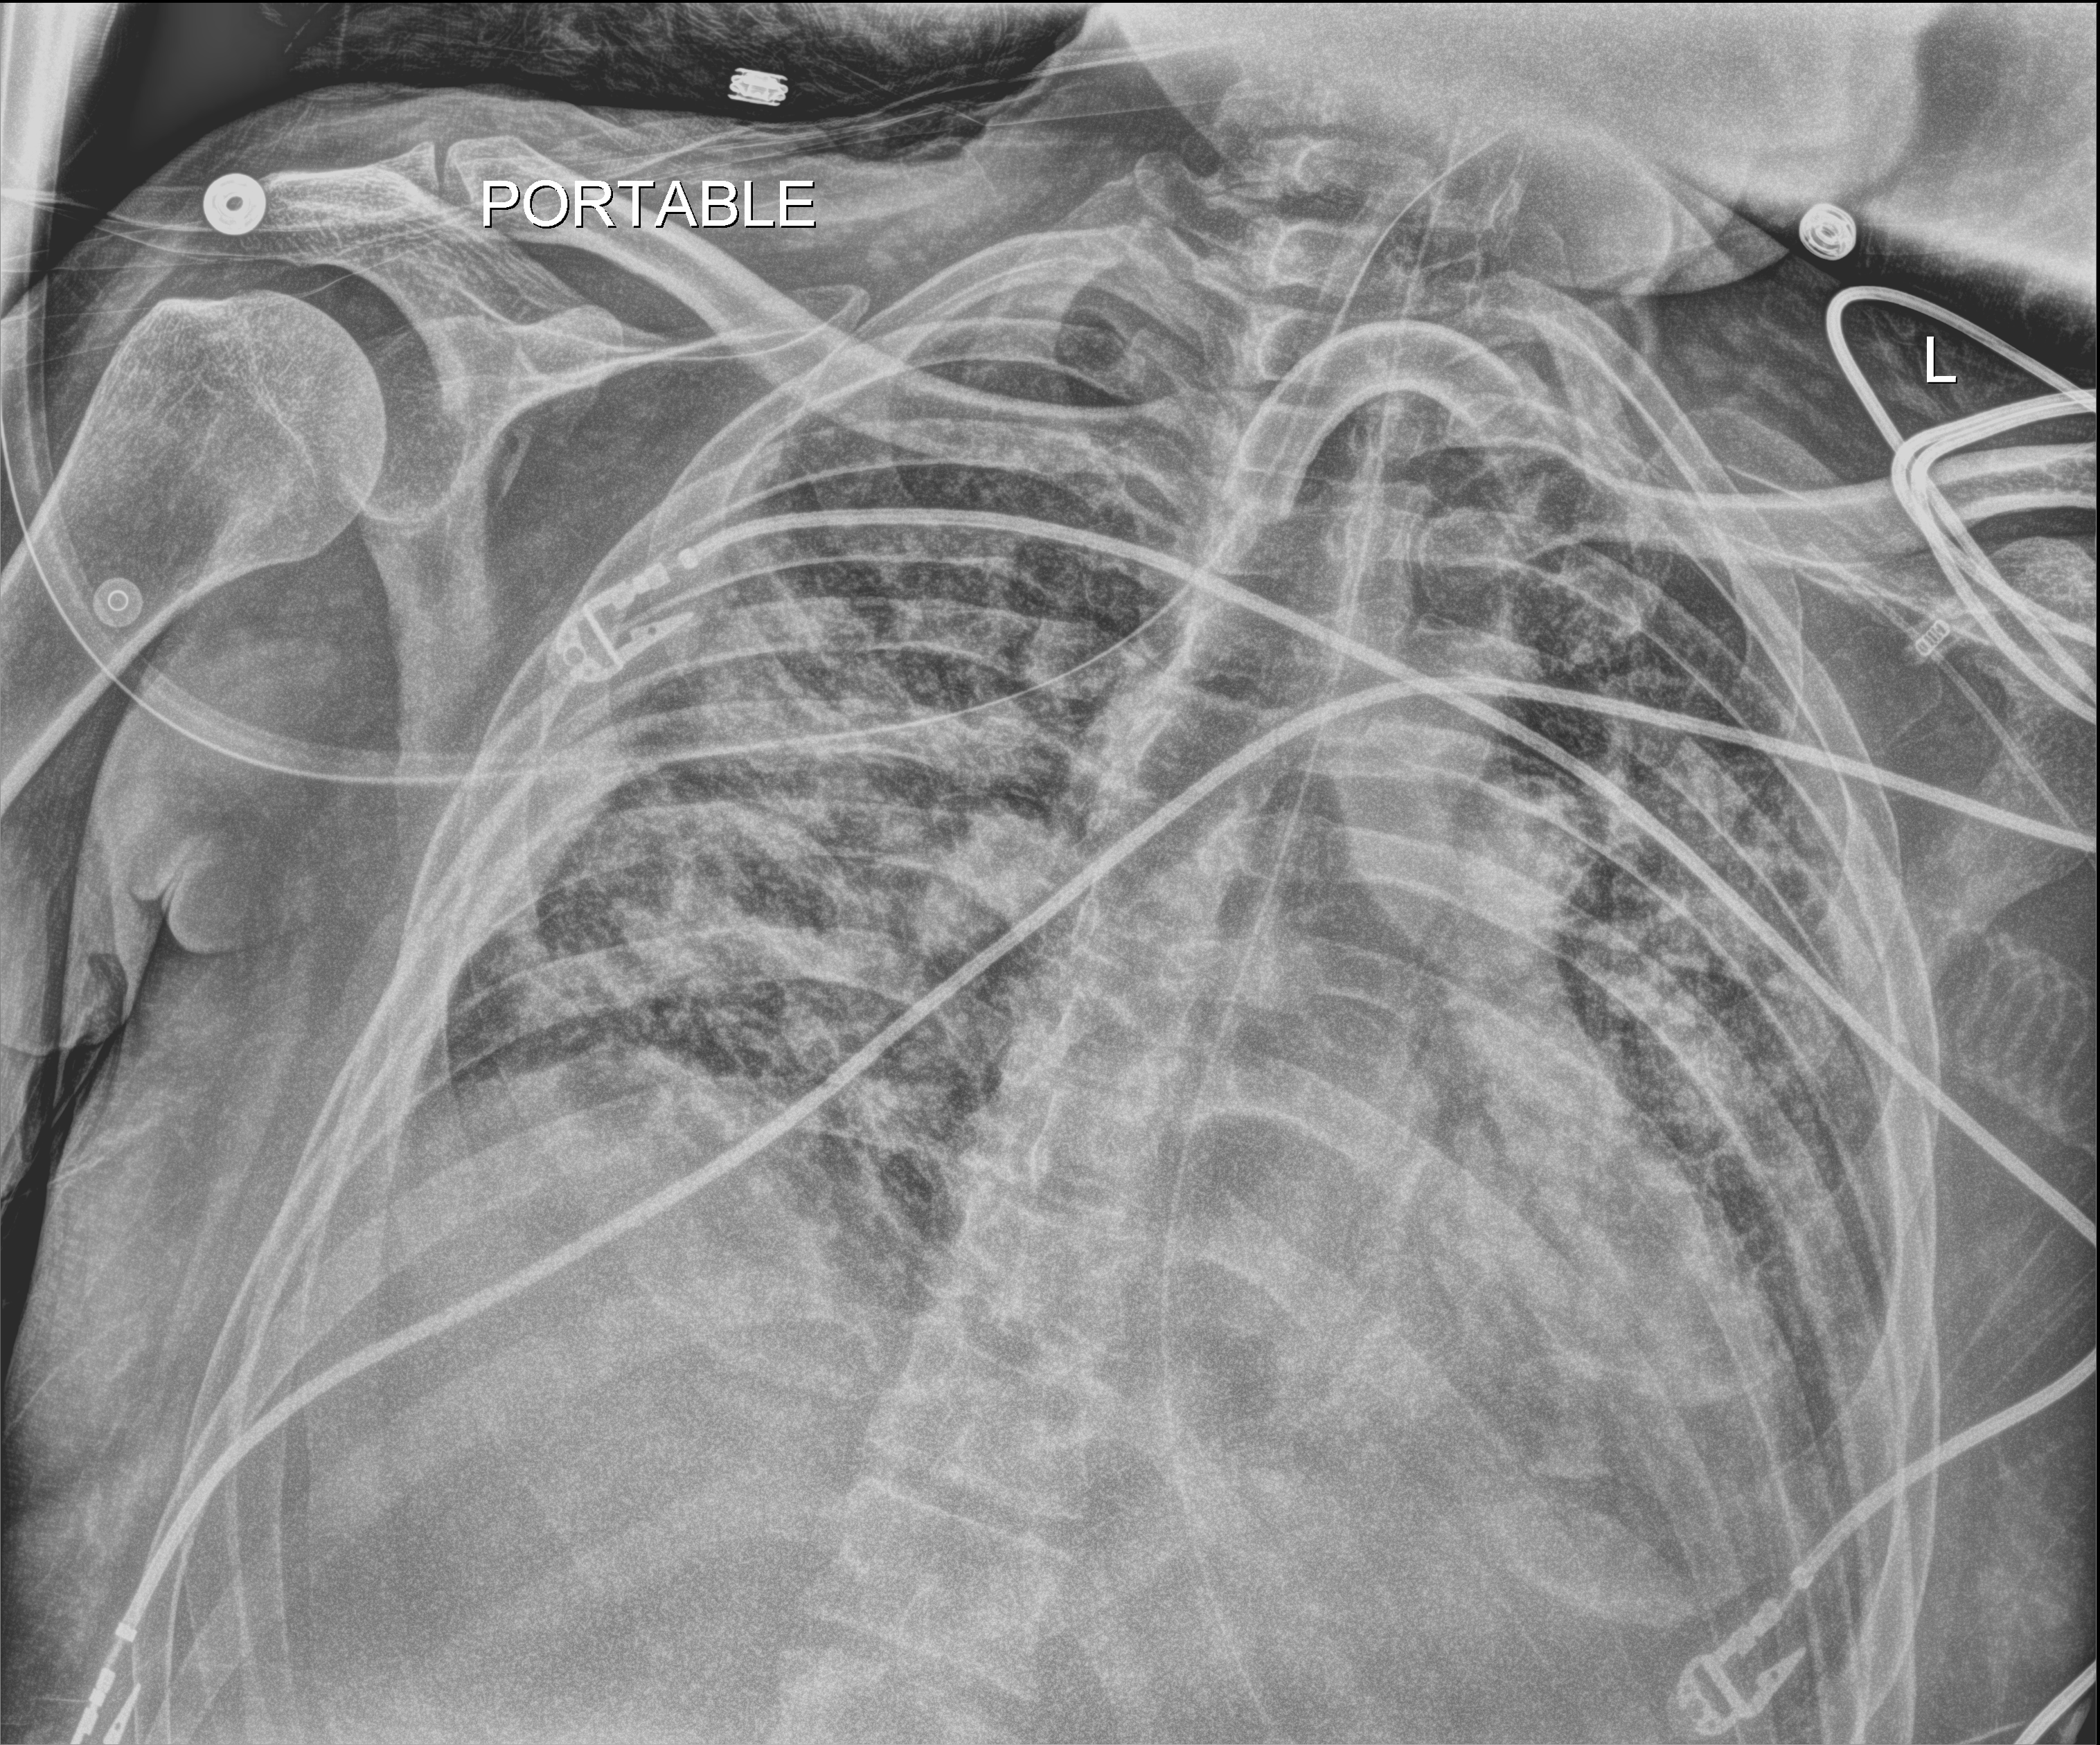
Bedside chest radiograph (digital radiography); anteroposterior (AP) projection. Male patient hospitalised with COVID-19, age 18–59 years.
Hospital-stay facts (about this admission, not read from this image; timing relative to this image not recorded):
- hypertension (admission record): no
- diabetes (admission record): no
- mechanically ventilated during this hospital stay: yes